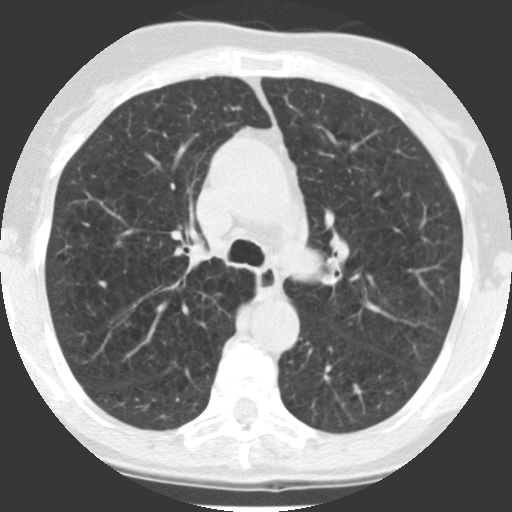
Chest CT (low-dose screening protocol), one axial image; first (baseline) screen; lung window (W 1500 / L -600 HU); 2.5 mm slice thickness; 512 × 512 image matrix. Female participant, aged 71 years at enrolment. Current smoker at enrolment.
- Expert reader's lesion annotation, box from (x=315, y=336) to (x=348, y=363) px.
- No non-calcified nodule or mass ≥4 mm was recorded by the screening reader at this exam.
- Later outcome: lung cancer diagnosed 802 days after this screen (after the third annual screen) — squamous cell carcinoma, NOS, left lower lobe, poorly differentiated (G3), stage IB (AJCC 6th edition), 40 mm at pathology.